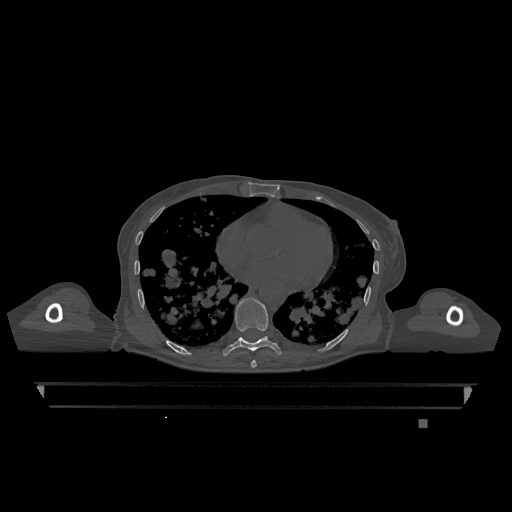
CT including the spine, one axial slice. Slice 690 of 1317 in the series (ordered by position). Bone window (W 1800 / L 400 HU). 0.5 mm slice thickness. 512 × 512 image matrix, field of view 500 × 500 mm. Female patient, age 74 years. From the clinical record (not read from this slice): primary cancer: lung; vertebrae with lytic lesions (as recorded): T1, T4, T5, T6, L4, L5.
Structures marked on this image (semi-automatic segmentation, software-assisted and operator-edited):
- T7 vertebra: bounding box (x1, y1, x2, y2) in pixels: (251, 360, 257, 368)
- T9 vertebra: (222, 297, 282, 356)